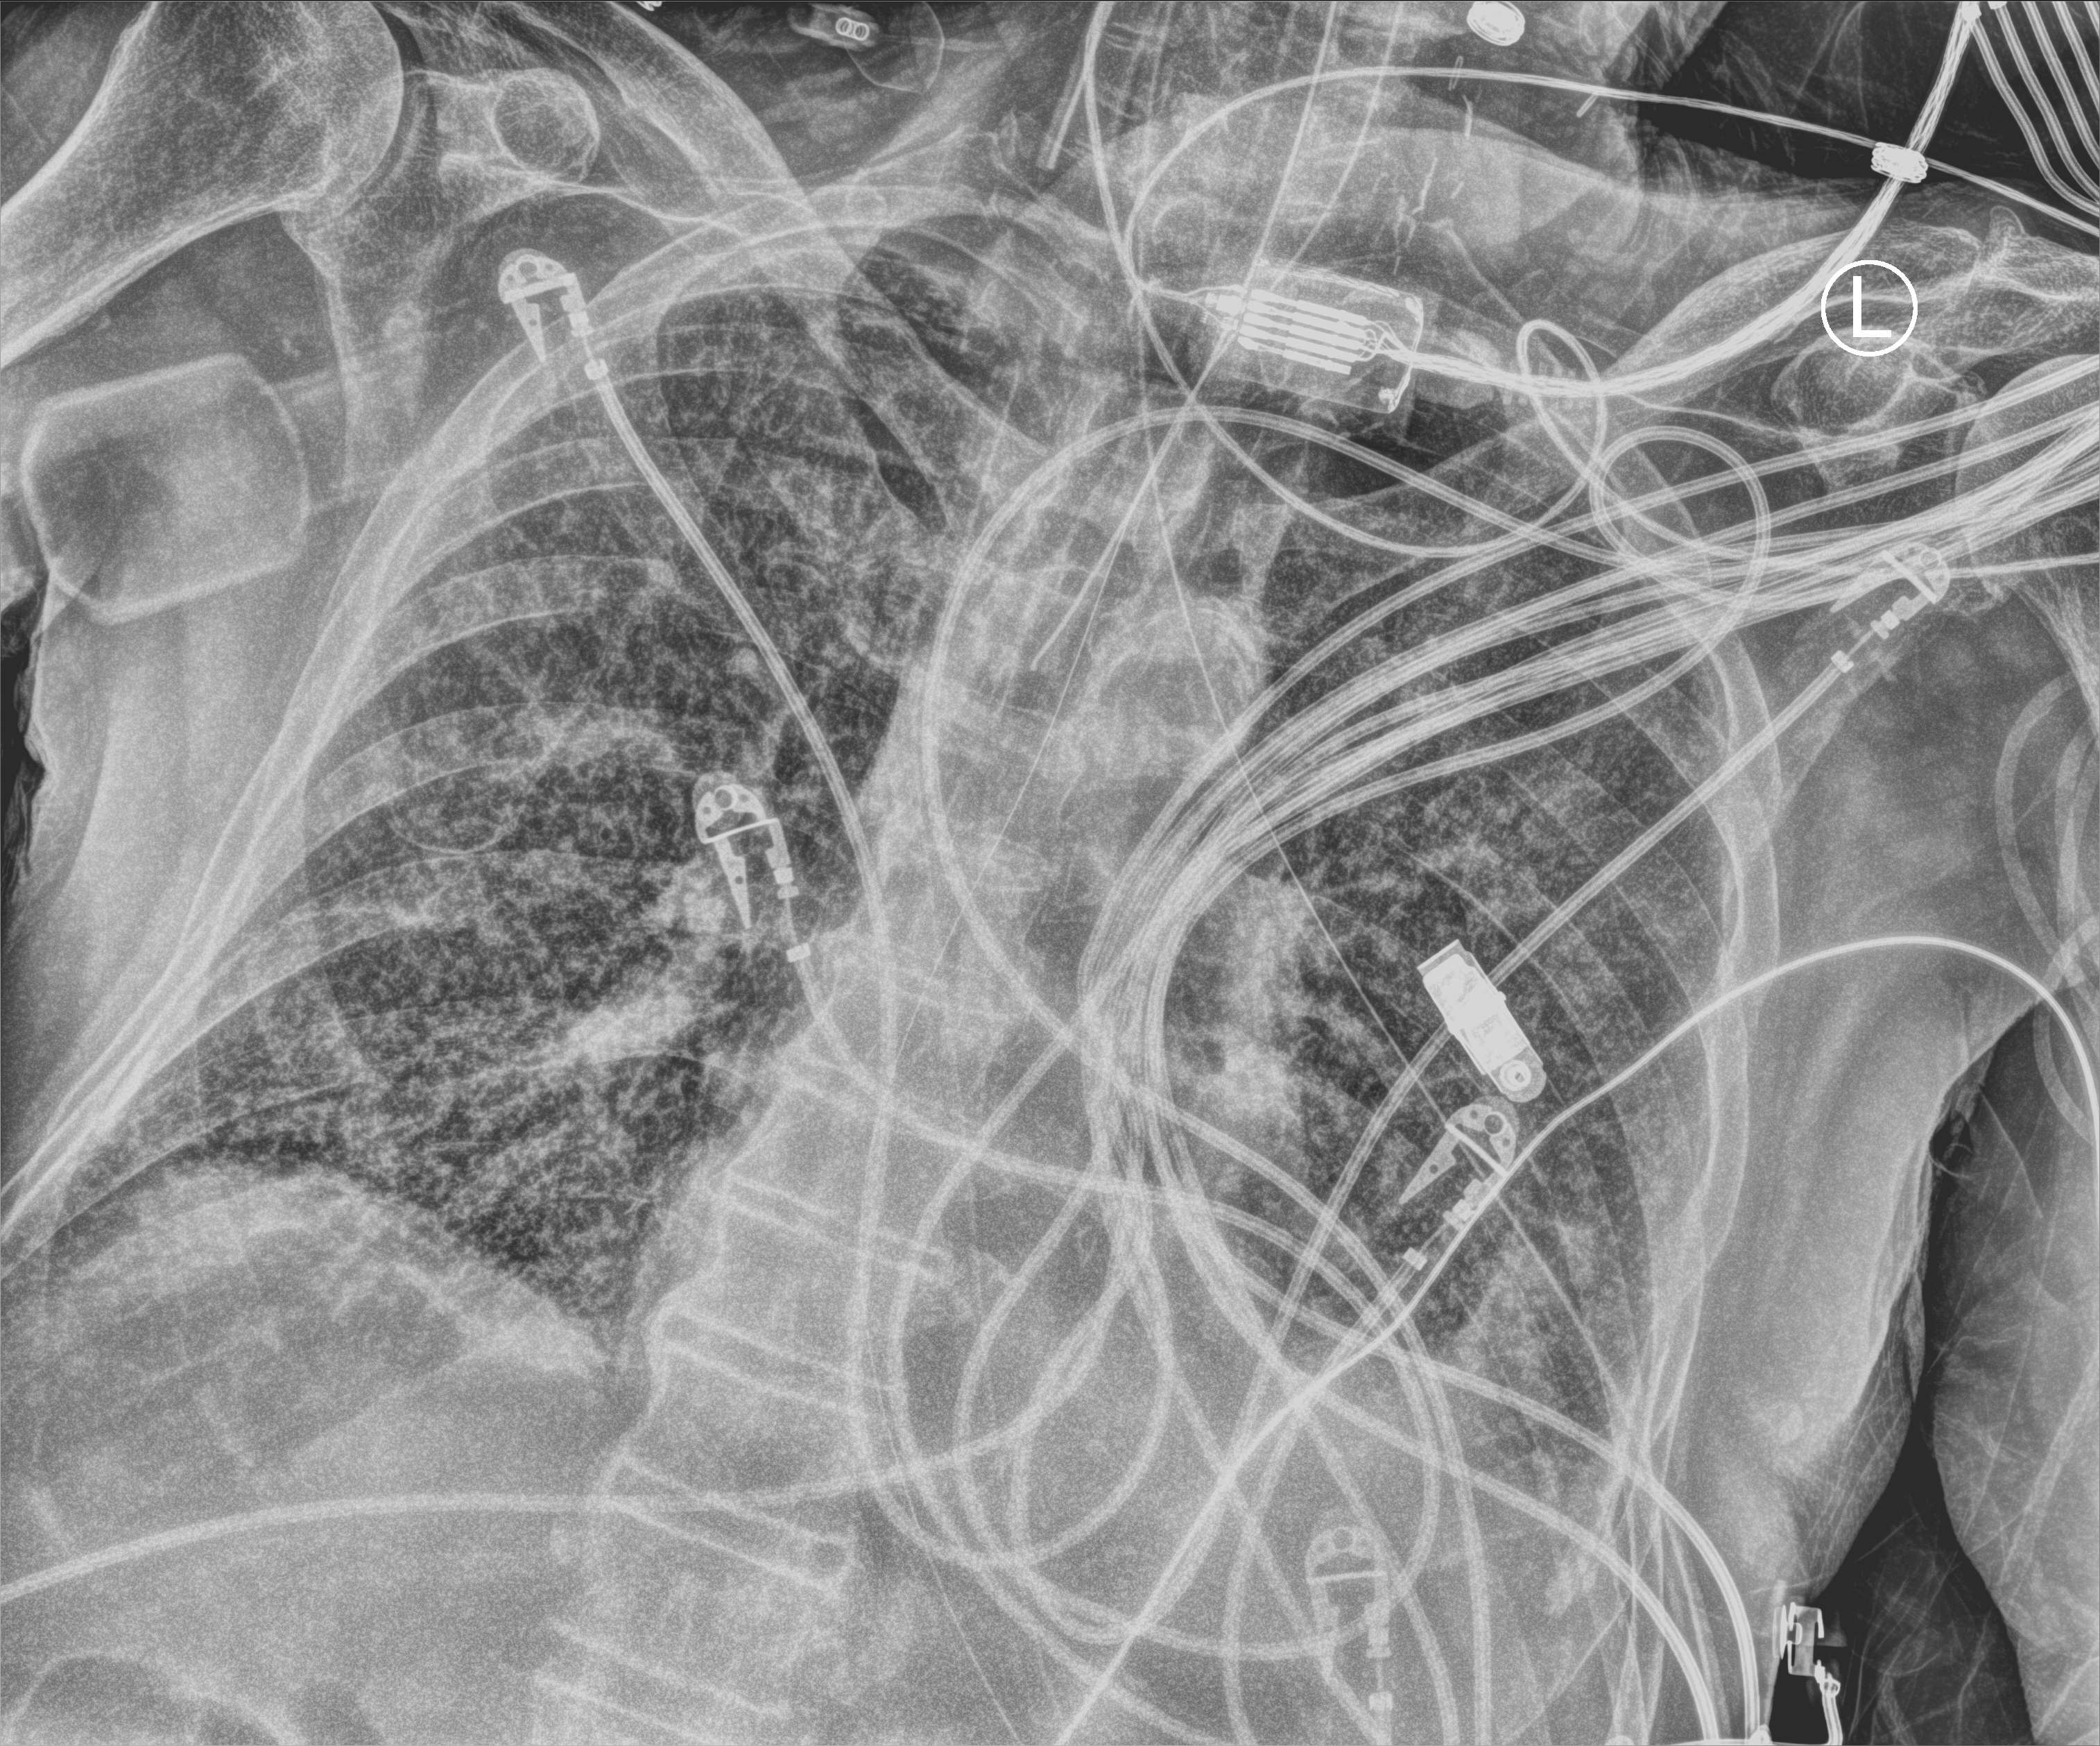
Bedside chest radiograph (computed radiography); anteroposterior (AP) projection. Patient hospitalised with COVID-19; male, aged 75–90 years.
From the hospital-stay record, not from the radiograph (when in the stay this image was taken is not recorded): mechanically ventilated during this hospital stay: yes.